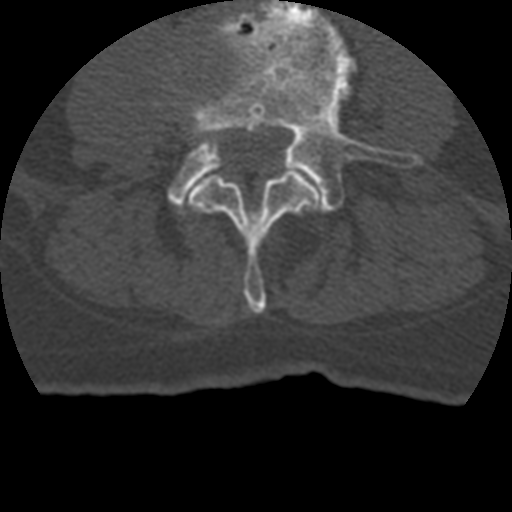
CT including the spine, one axial slice; position 76 of 399 along the scan axis; reconstruction kernel STANDARD; 120 kVp; bone window (W 1800 / L 400 HU); 1.25 mm slice thickness; 512 × 512 image matrix, field of view 160 × 160 mm. Patient age 69 years. Case-level facts recorded for this patient, not image findings: primary cancer: prostate.
Structures marked on this image (semi-automatically segmented with operator editing):
- L3 vertebra: bounding box (x1, y1, x2, y2) in pixels: (189, 170, 319, 314)
- L4 vertebra: (168, 0, 423, 213)